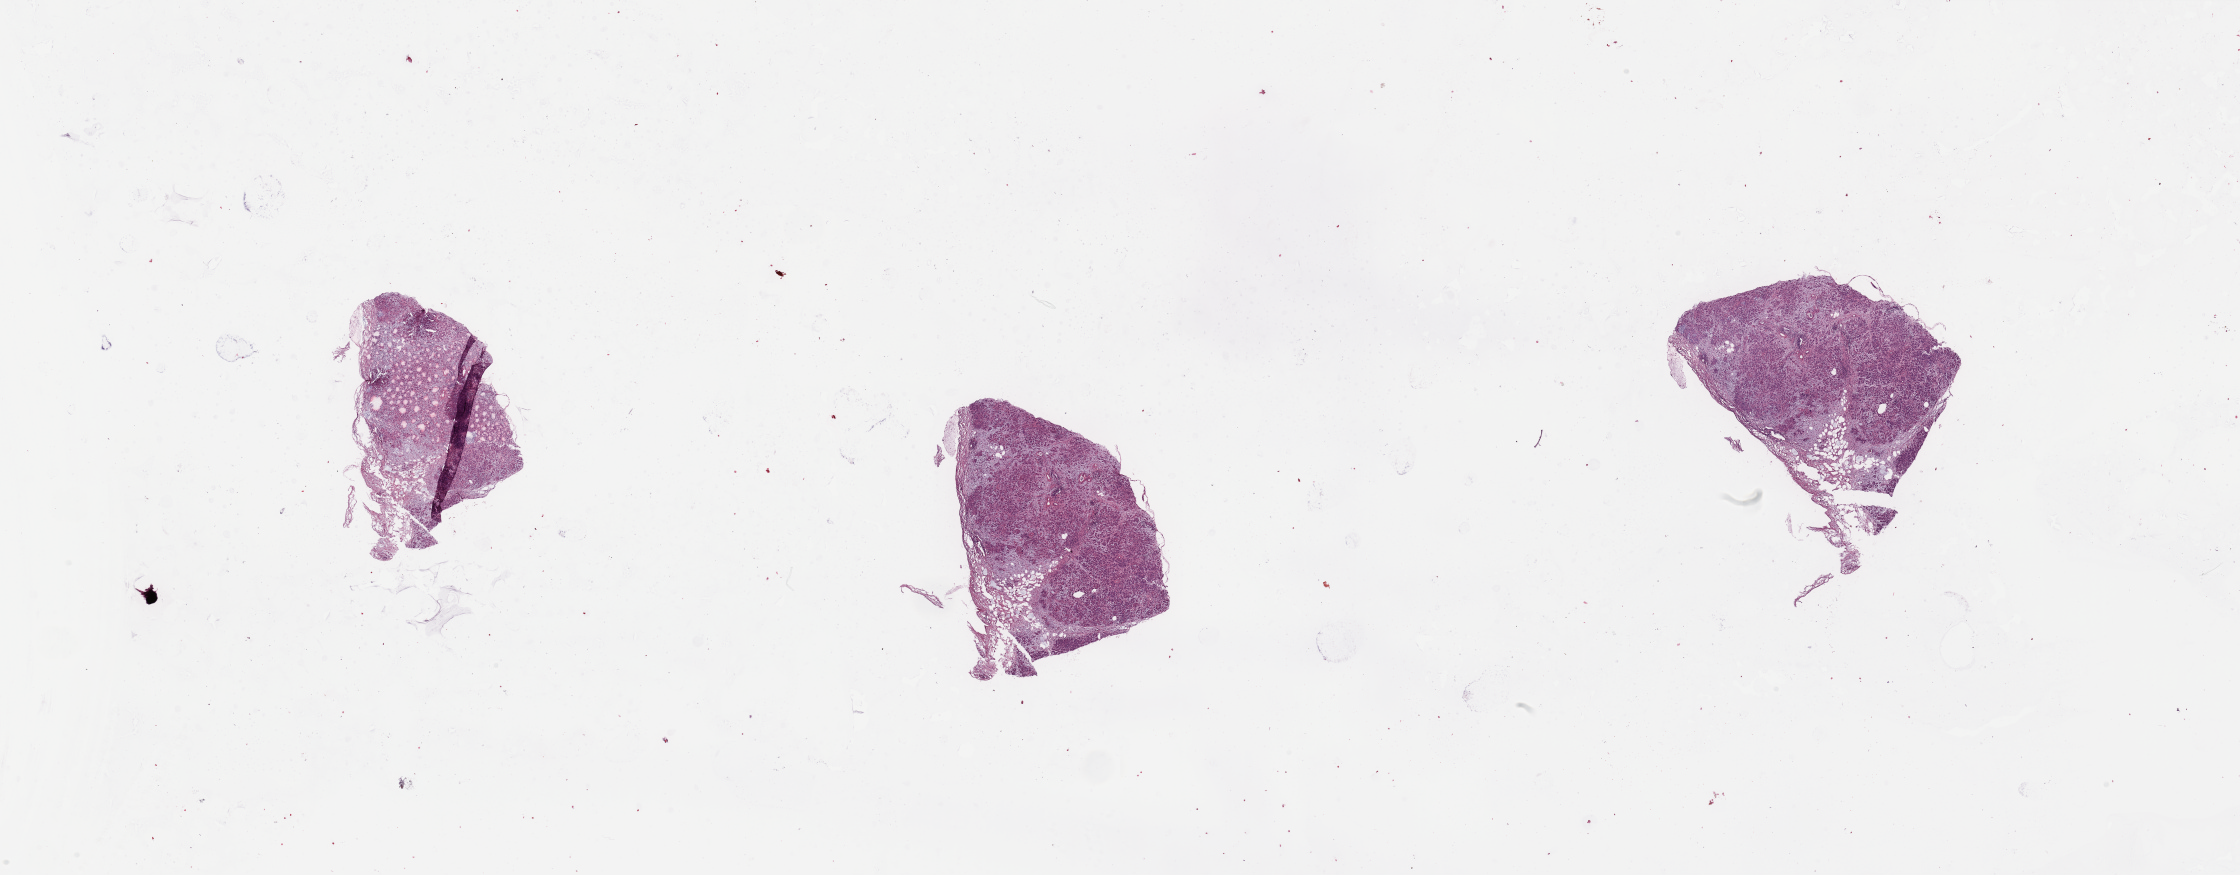
Whole-slide histology image, Hematoxylin and eosin (H&E) stained — low-resolution overview of the scanned area, about 35.4 x 13.8 mm, tumour tissue sample, pancreas. Female, 65 y/o.
Primary tumour site (as recorded): head. Patient diagnosis (cohort enrolment): ductal adenocarcinoma (pancreas).